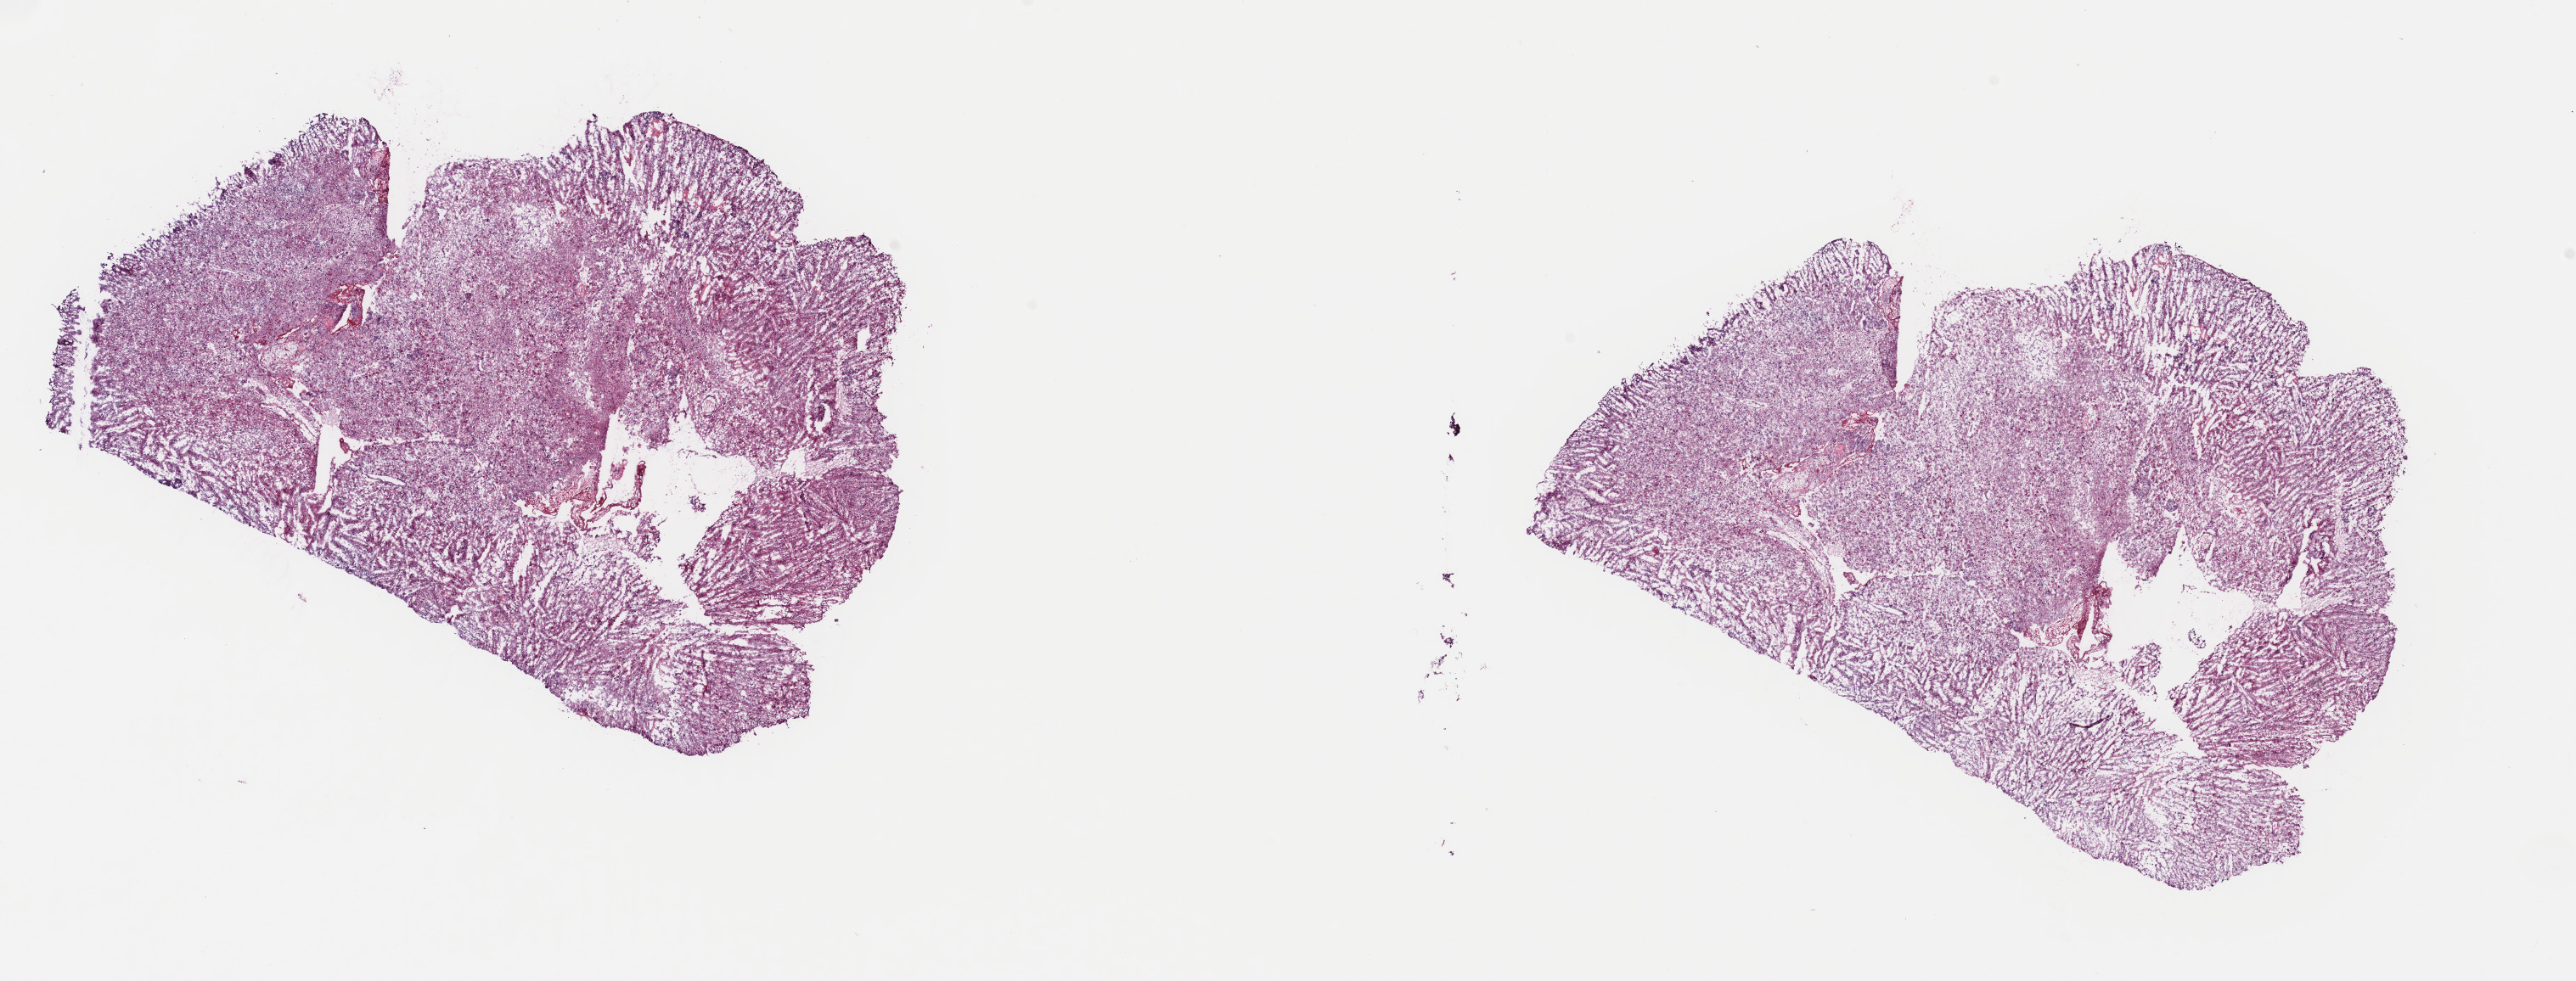
Digitized Hematoxylin and eosin (H&E) stained tissue section (whole slide) — shown as a low-resolution overview of the whole scanned area (about 23.9 x 9.1 mm, acquisition: 40x scan), frozen section from the top of the tissue portion, brain, primary tumour sample. Patient: female, age at initial diagnosis 53 years. Pathologist review of this section (percent, as recorded): tumour cells 40%, tumour nuclei 80%, normal cells 20%, stromal cells 40%, necrosis 0%. Inflammatory infiltration, as recorded: lymphocyte infiltration 10%, monocyte infiltration 5%, neutrophil infiltration 0%.
Pathologic diagnosis: Glioblastoma.